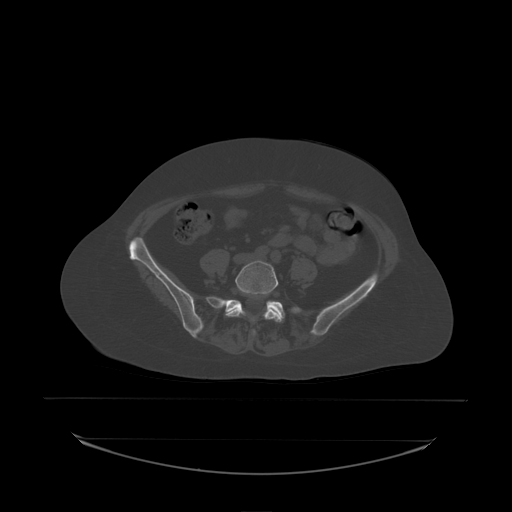
CT including the spine, one axial slice; position 36 of 242 along the scan axis; bone window (W 1800 / L 400 HU); 512 × 512 image matrix, field of view 500 × 500 mm. Patient: female, 53 years. Case-level facts recorded for this patient, not image findings: primary cancer: lung; vertebrae with lytic lesions (as recorded): T7, L1.
Annotated regions visible in this slice (semi-automatically segmented with operator editing):
- L5 vertebra: bounding box <226,261,281,335> (left, top, right, bottom; pixels)